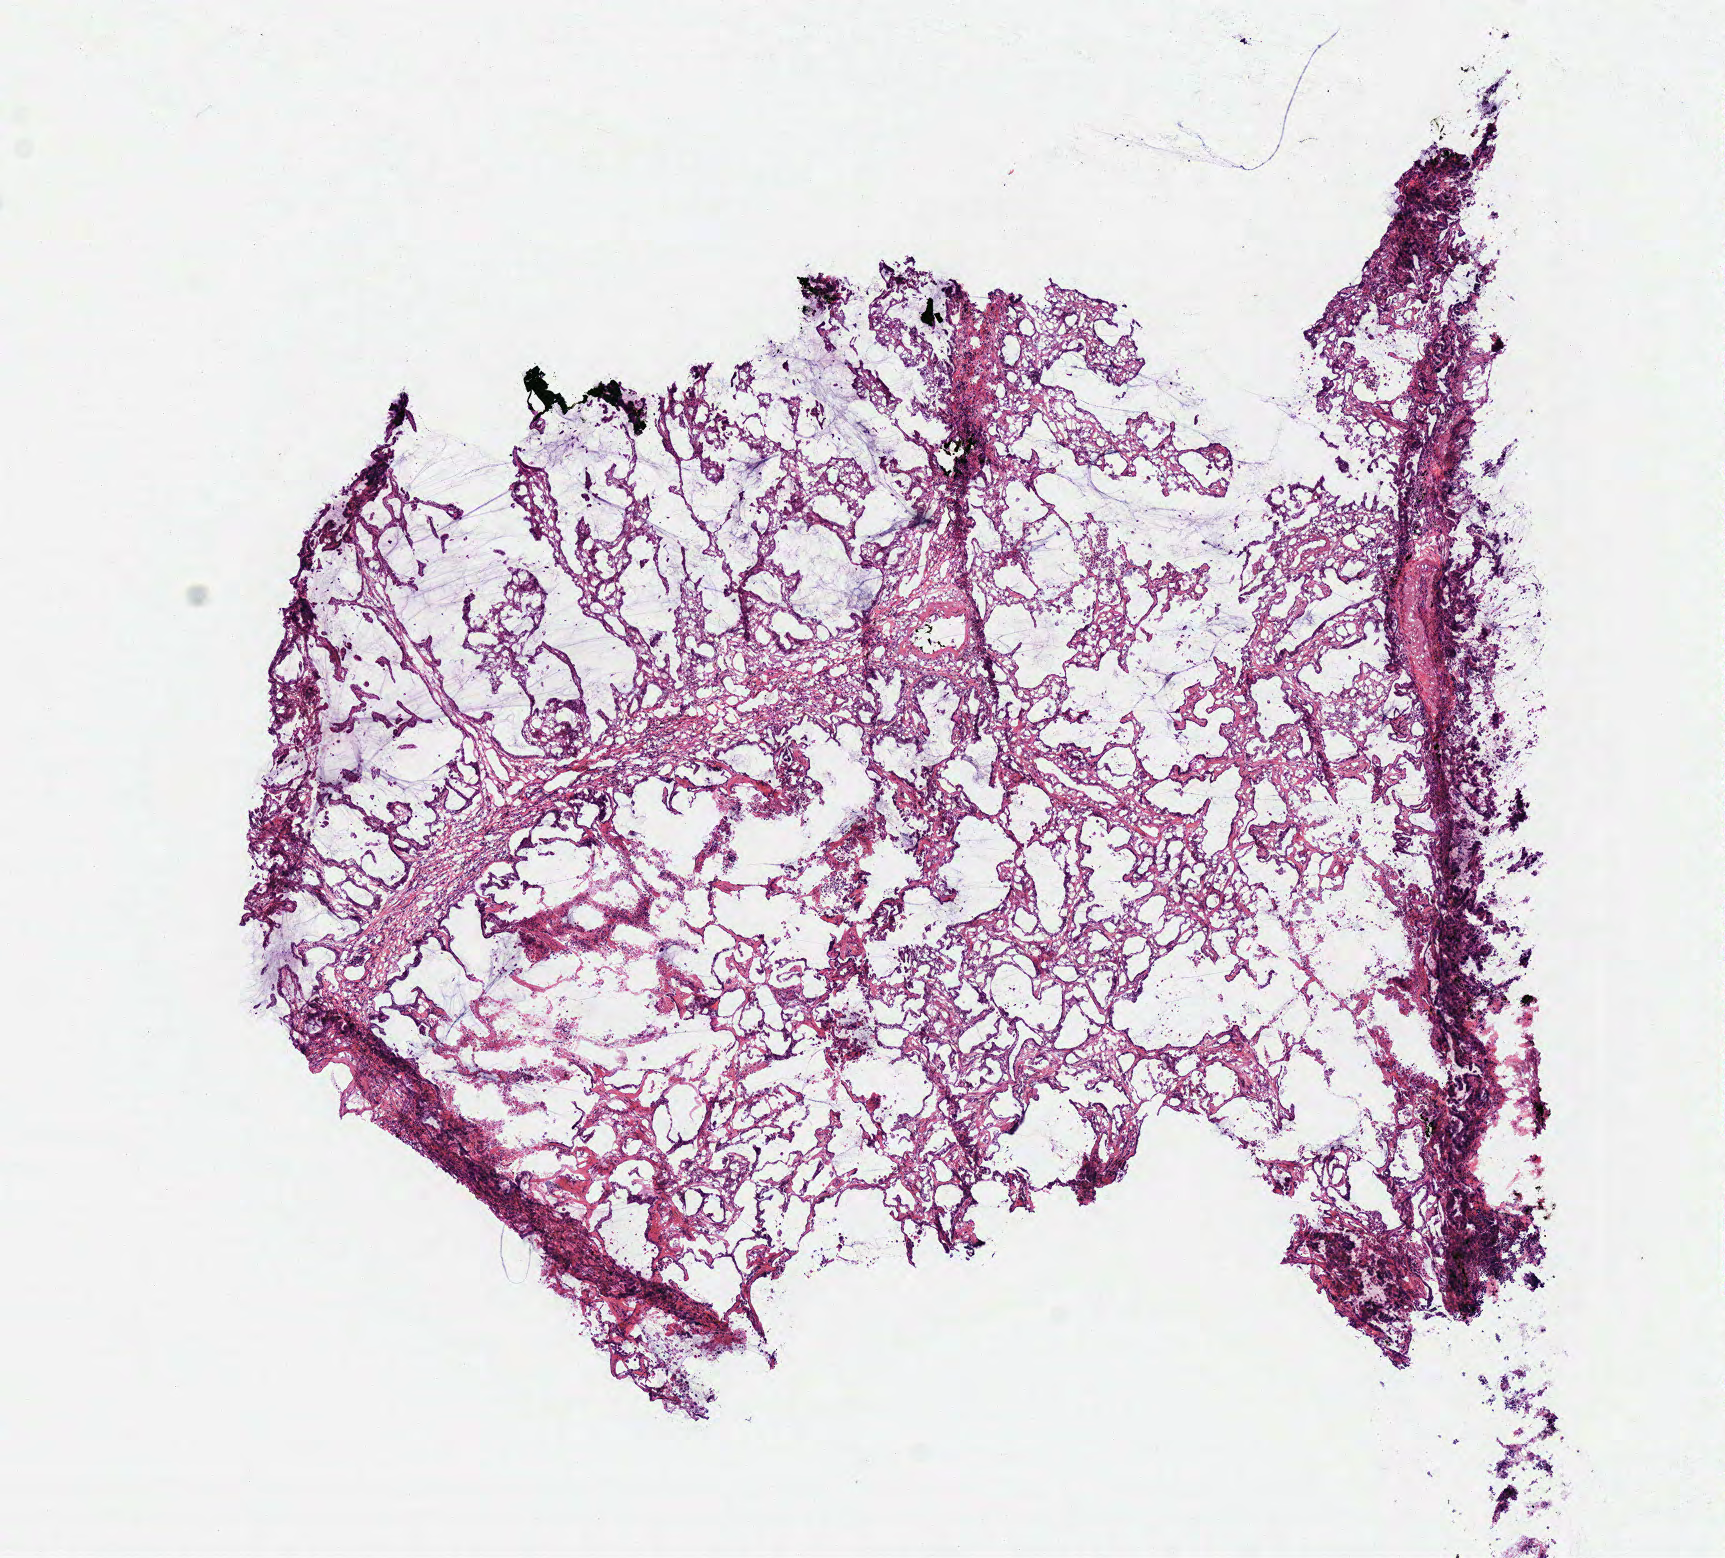
Whole-slide histology image, H&E-stained — shown as a low-resolution overview of the whole scanned area (about 6.8 x 6.1 mm, from a 40x scan); frozen section from the top of the tissue portion; lung, primary tumour sample. Patient: male, age at initial diagnosis 84 years. Pathologist review of this section (percent, as recorded): tumour cells 65%, tumour nuclei 70%, normal cells 0%, stromal cells 15%, necrosis 20%.
AJCC pathologic stage: IIB (6th edition). Pathologic diagnosis: Adenocarcinoma, NOS (lower lobe, lung).